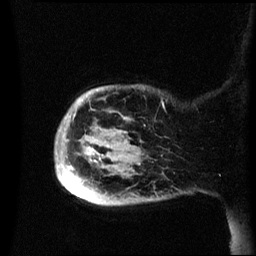
Breast MRI (dynamic contrast-enhanced), one sagittal slice; position 7 of 60 along the scan axis; dynamic contrast-enhanced series, image 2 of 3 at this slice position (ordered by acquisition); 1.5 T; TE 4.2 ms, TR 8.4 ms; 2.4 mm slice thickness; 256 × 256 image matrix, field of view 230 × 230 mm. Female patient, age 49 years.
Annotated regions visible in this slice (semi-automatically segmented with operator editing):
- analysis volume of interest (the breast-tissue region the enhancement analysis was run in; not a lesion): bounding box <55,85,173,206> (left, top, right, bottom; pixels)
- tumour enhancement mask (voxels above the 70 % enhancement threshold inside the analysis volume of interest): <61,181,83,199>